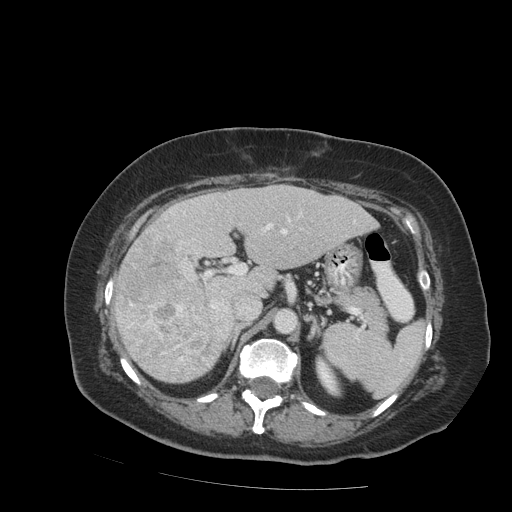
Contrast-enhanced abdominal CT (liver protocol), one axial slice. Position 50 of 99 along the scan axis. Soft-tissue window (W 400 / L 40 HU). 512 × 512 image matrix, field of view 400 × 400 mm. Case-level facts recorded for this patient, not image findings: diagnosis: hepatocellular carcinoma (patient treated with transarterial chemoembolisation; whether this scan precedes or follows treatment is not stated here); TNM stage (as recorded): Stage-IVB; Child-Pugh class: A.
Outlined on this slice (semi-automatic segmentation, software-assisted and operator-edited):
- liver parenchyma outside the tumour (the mass and vessels are separate outlines, so this box may not span the whole liver): bounding box [x1, y1, x2, y2] px = [114, 184, 378, 382]
- mass: [114, 228, 228, 381]
- liver vessels: [170, 211, 290, 312]